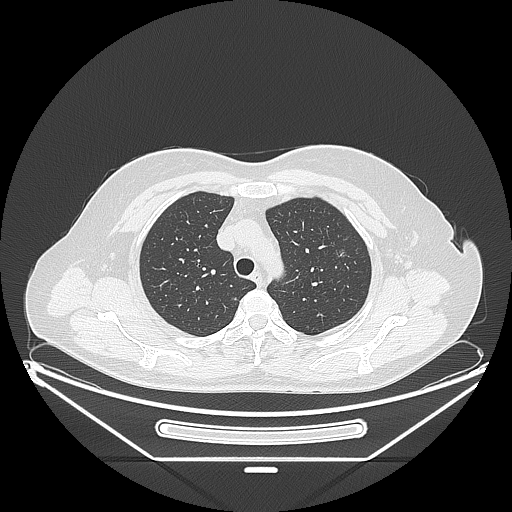
Chest CT, one axial slice. Slice 170 of 226 in the series (ordered by position). Reconstruction kernel LUNG. 120 kVp. Lung window (W 1500 / L -600 HU). 1.25 mm slice thickness. 512 × 512 image matrix, field of view 447 × 447 mm. Patient: female, 54 years. From the clinical record (not read from this slice): clinical TNM (as recorded): T1c N0 M0.
Structures marked on this image (bounding box drawn by a radiologist):
- lung tumour (recorded histology: adenocarcinoma): bounding box (x1, y1, x2, y2) in pixels: (336, 244, 354, 264)